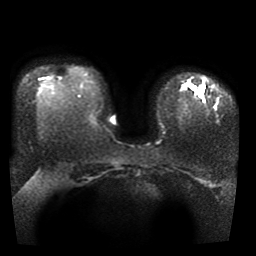
Breast MRI, one axial slice. Slice 29 of 41 in the series (ordered by position). Diffusion-weighted series; image 2 of 4 stored at this slice position (different b-values; order by instance number). 1.5 T. 5 mm slice thickness. 256 × 256 image matrix, field of view 330 × 330 mm. Female patient.
Annotated regions visible in this slice (outlined manually by an expert reader):
- tumour on diffusion-weighted imaging: box from (x=189, y=84) to (x=203, y=98) px